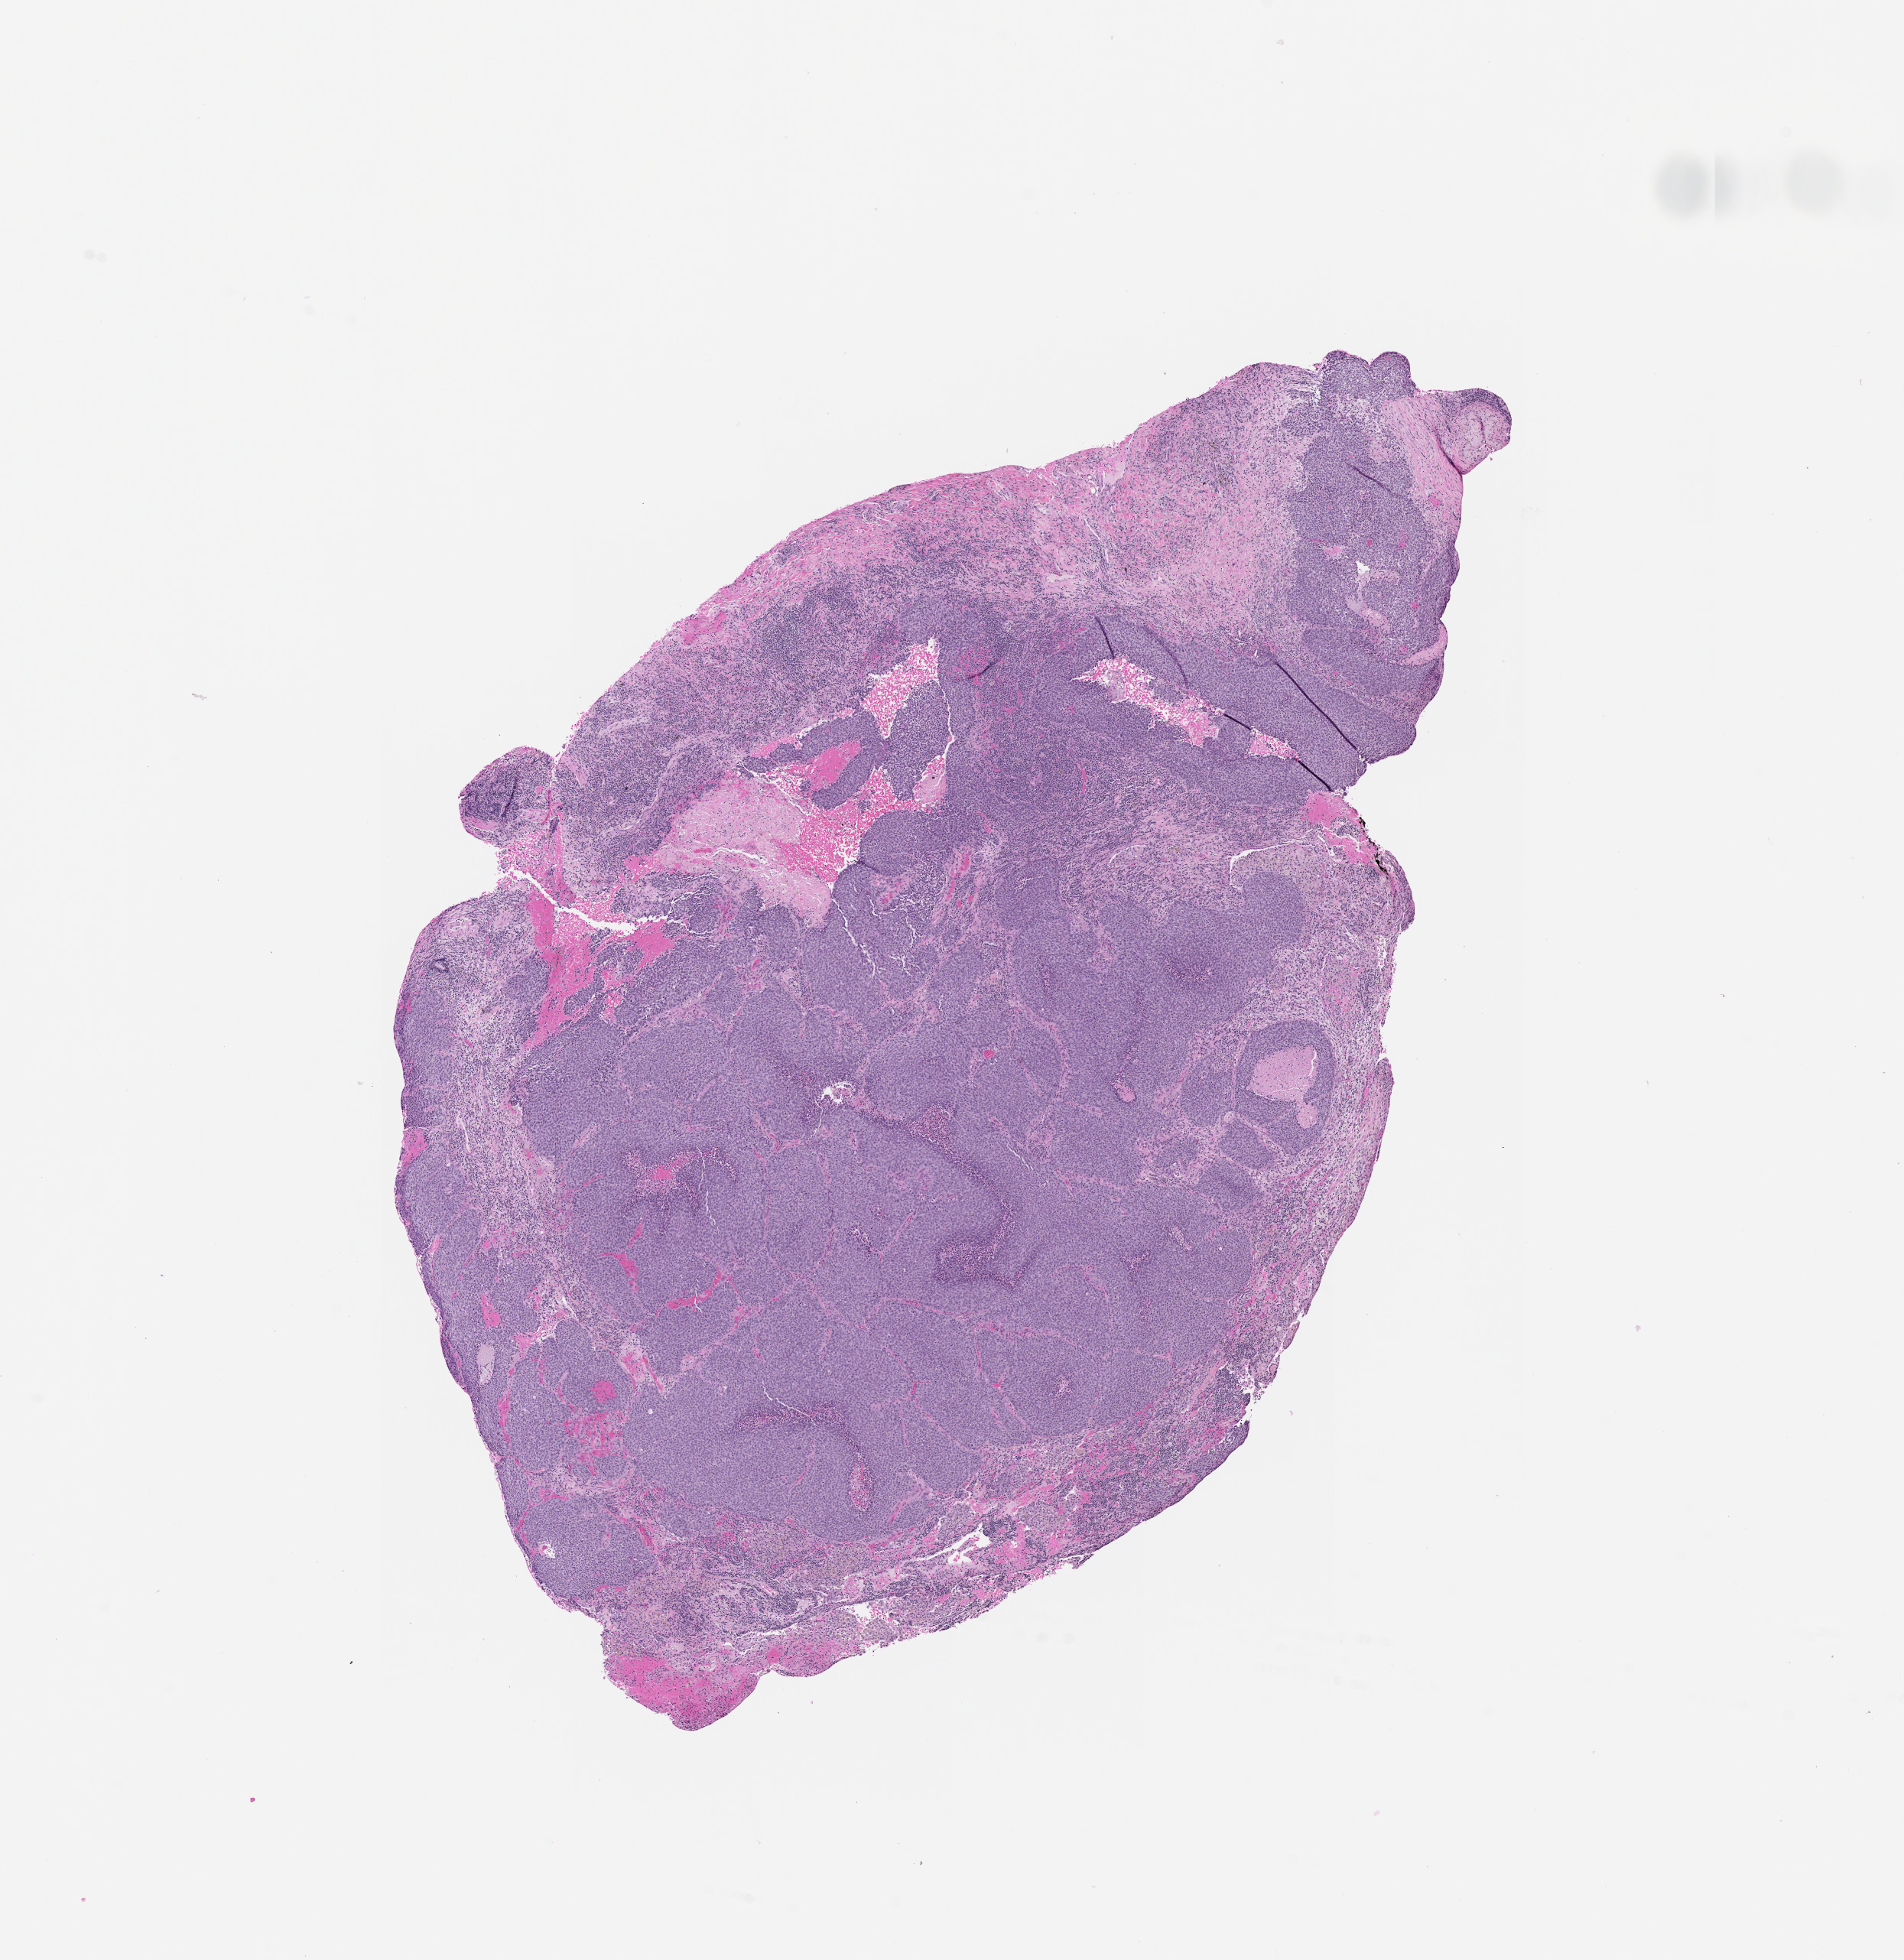
H&E-stained whole-slide image — low-resolution overview of the scanned area, about 10.0 x 10.3 mm (from a 20x scan). Tumour tissue sample, lung. 68-year-old male patient.
Patient diagnosis (cohort enrolment): squamous cell carcinoma (lung).